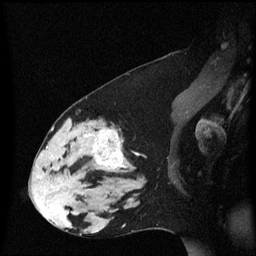
Breast MRI (dynamic contrast-enhanced), one sagittal slice. Position 34 of 60 along the scan axis. Dynamic contrast-enhanced series, image 2 of 3 at this slice position (ordered by acquisition). 1.5 T. TE 4.2 ms, TR 8.4 ms. 256 × 256 image matrix, field of view 210 × 210 mm. Patient: female, 33 years. From the clinical record (not read from this slice): setting: breast cancer imaged before/during neoadjuvant chemotherapy; receptor status: triple-negative.
Annotated regions visible in this slice (semi-automatically segmented with operator editing):
- analysis volume of interest (the breast-tissue region the enhancement analysis was run in; not a lesion): bounding box [x1, y1, x2, y2] px = [44, 123, 139, 189]
- tumour enhancement mask (voxels above the 70 % enhancement threshold inside the analysis volume of interest): [57, 130, 124, 171]